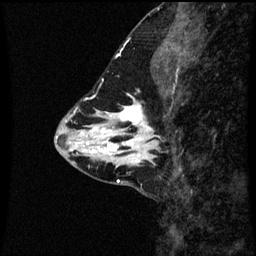
Breast MRI (dynamic contrast-enhanced), one sagittal slice; position 22 of 60 along the scan axis; dynamic contrast-enhanced series, image 2 of 3 at this slice position (ordered by acquisition); 1.5 T; TE 4.2 ms, TR 8.9 ms; 256 × 256 image matrix. Female patient, age 43 years. Case-level facts recorded for this patient, not image findings: setting: breast cancer imaged before/during neoadjuvant chemotherapy; receptor status: HR-positive, HER2-negative.
Outlined on this slice (semi-automatically segmented with operator editing):
- analysis volume of interest (the breast-tissue region the enhancement analysis was run in; not a lesion): box from (x=110, y=100) to (x=174, y=163) px
- tumour enhancement mask (voxels above the 70 % enhancement threshold inside the analysis volume of interest): (x=110, y=100)–(x=157, y=163)